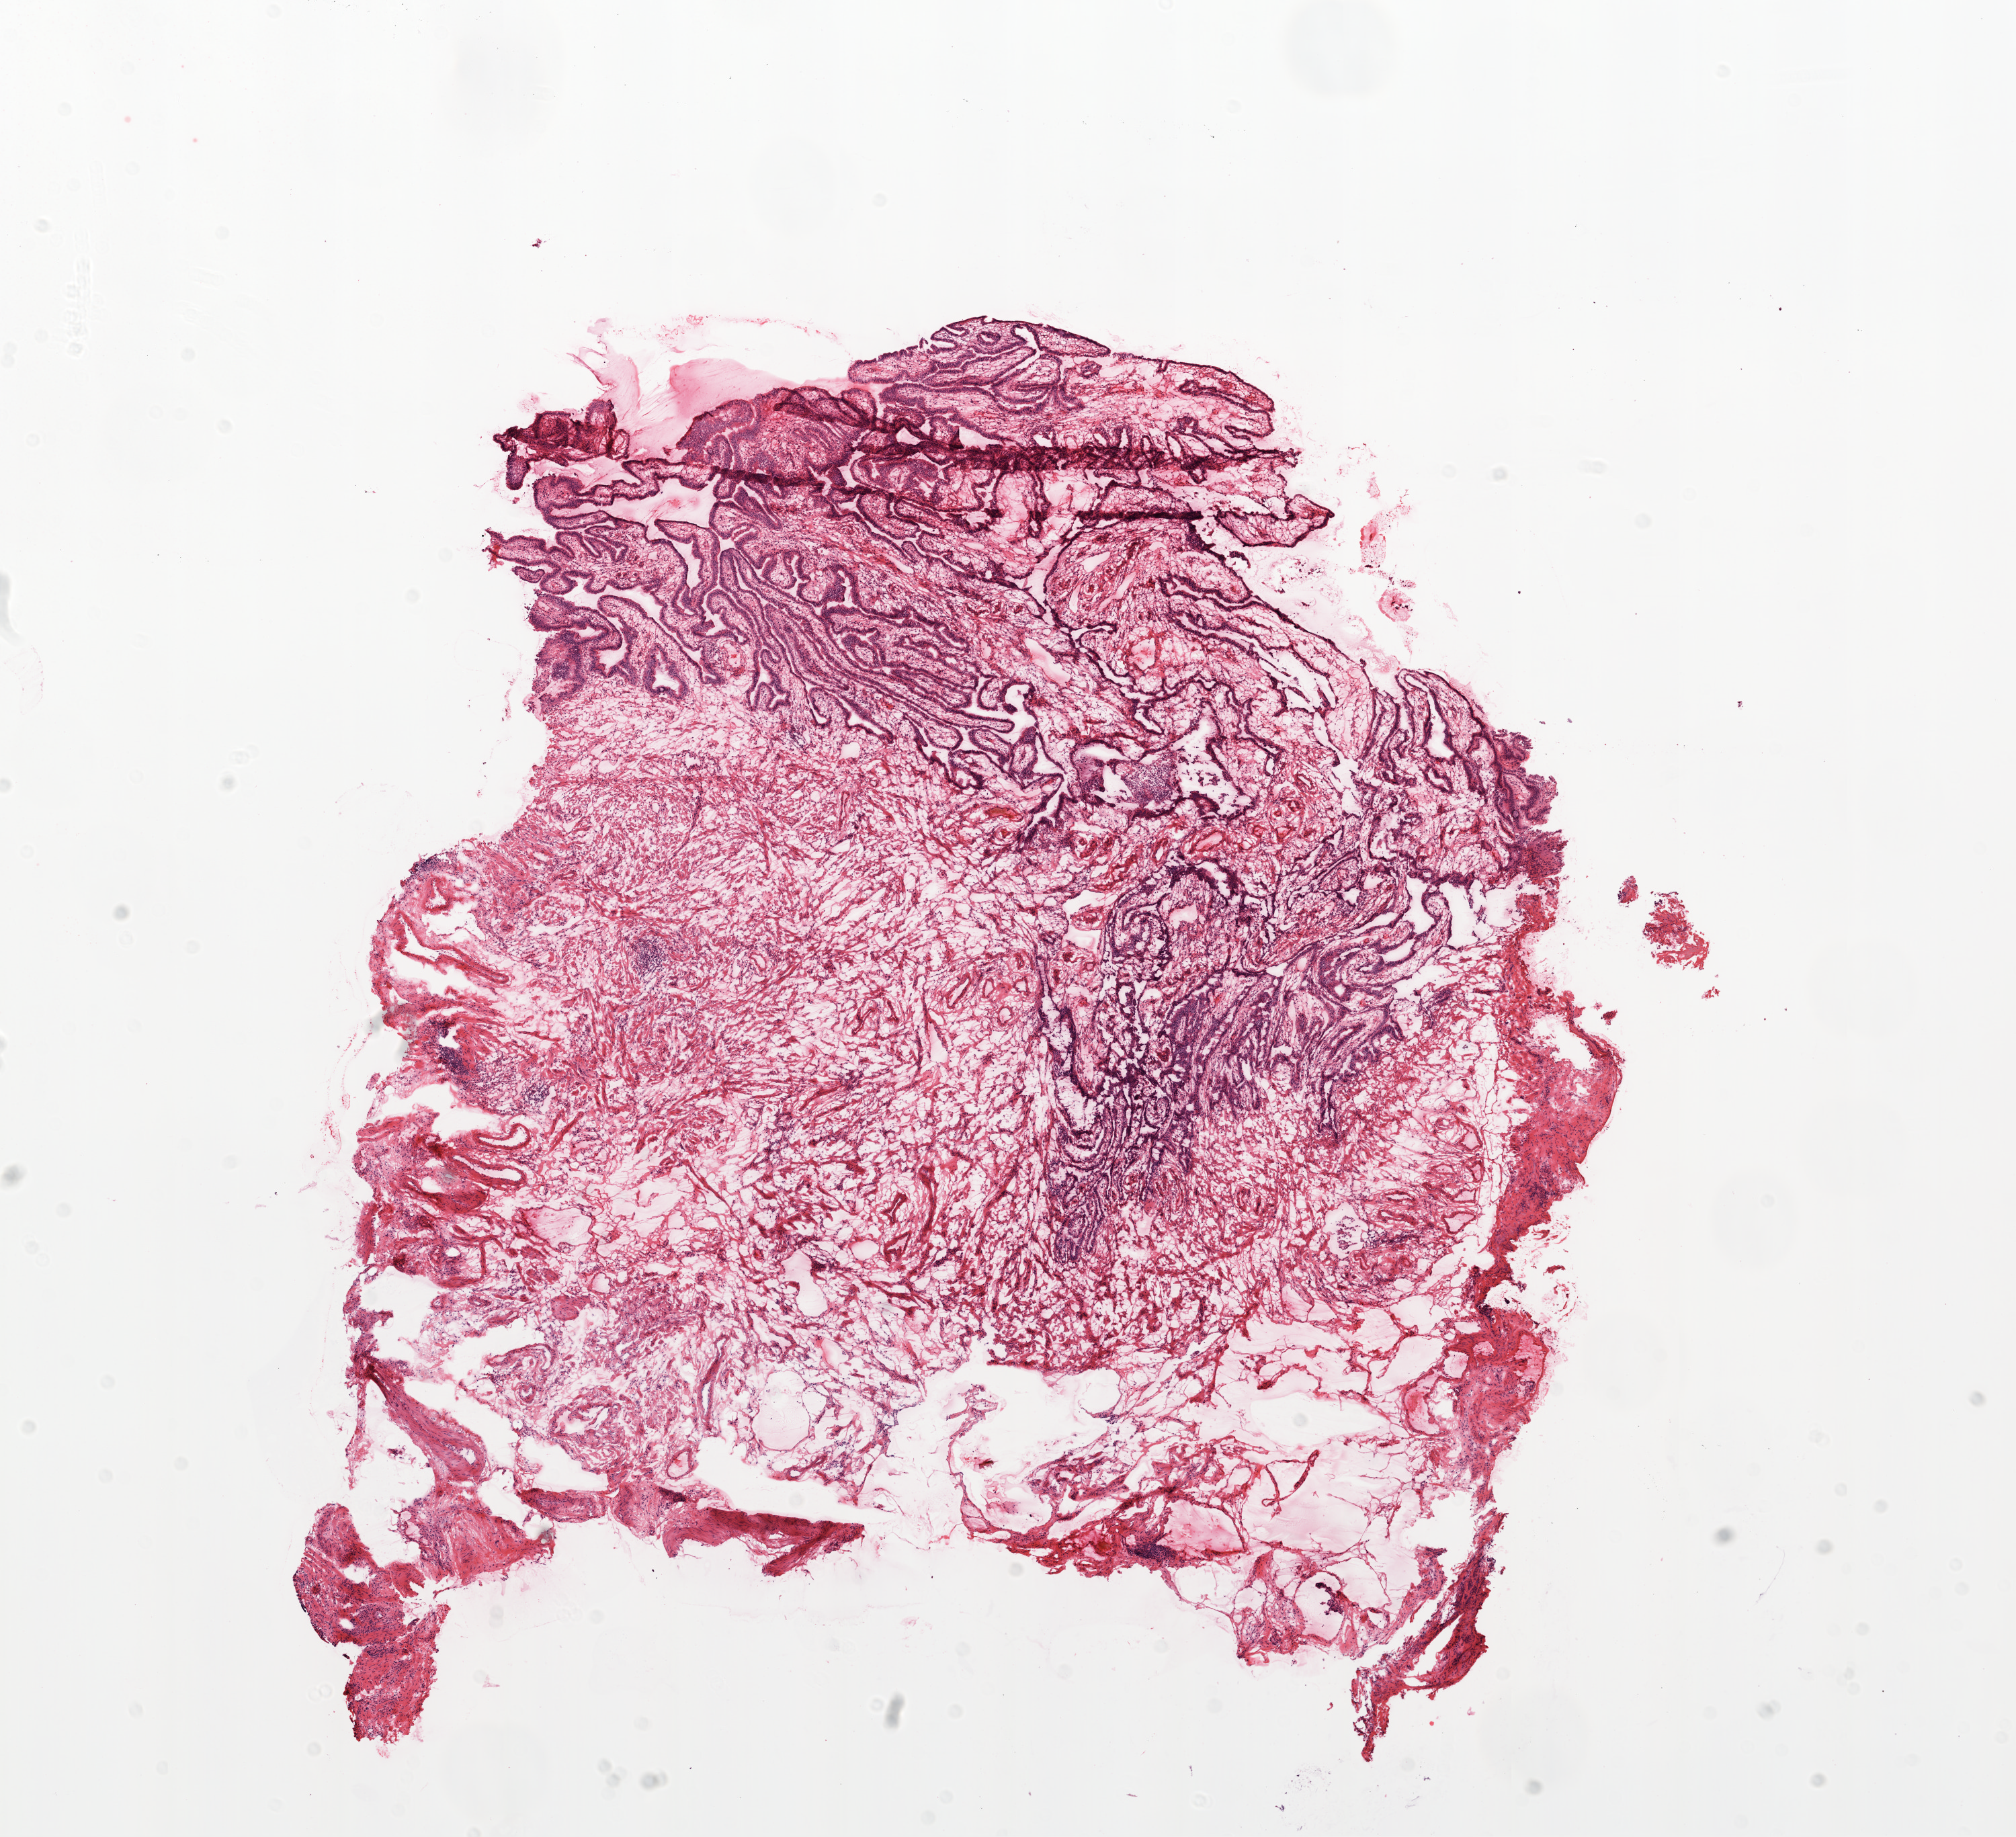
Digitized H&E tissue section (whole slide), shown as a low-resolution overview of the whole scanned area (about 12.0 x 11.0 mm, slide scanned at 20x); frozen section; ovary, solid tissue normal (non-tumour tissue) sample. Female patient; age at initial diagnosis 48 years.
• this section: solid tissue normal (non-tumour) sample from the same patient
• patient diagnosis: Serous cystadenocarcinoma, NOS